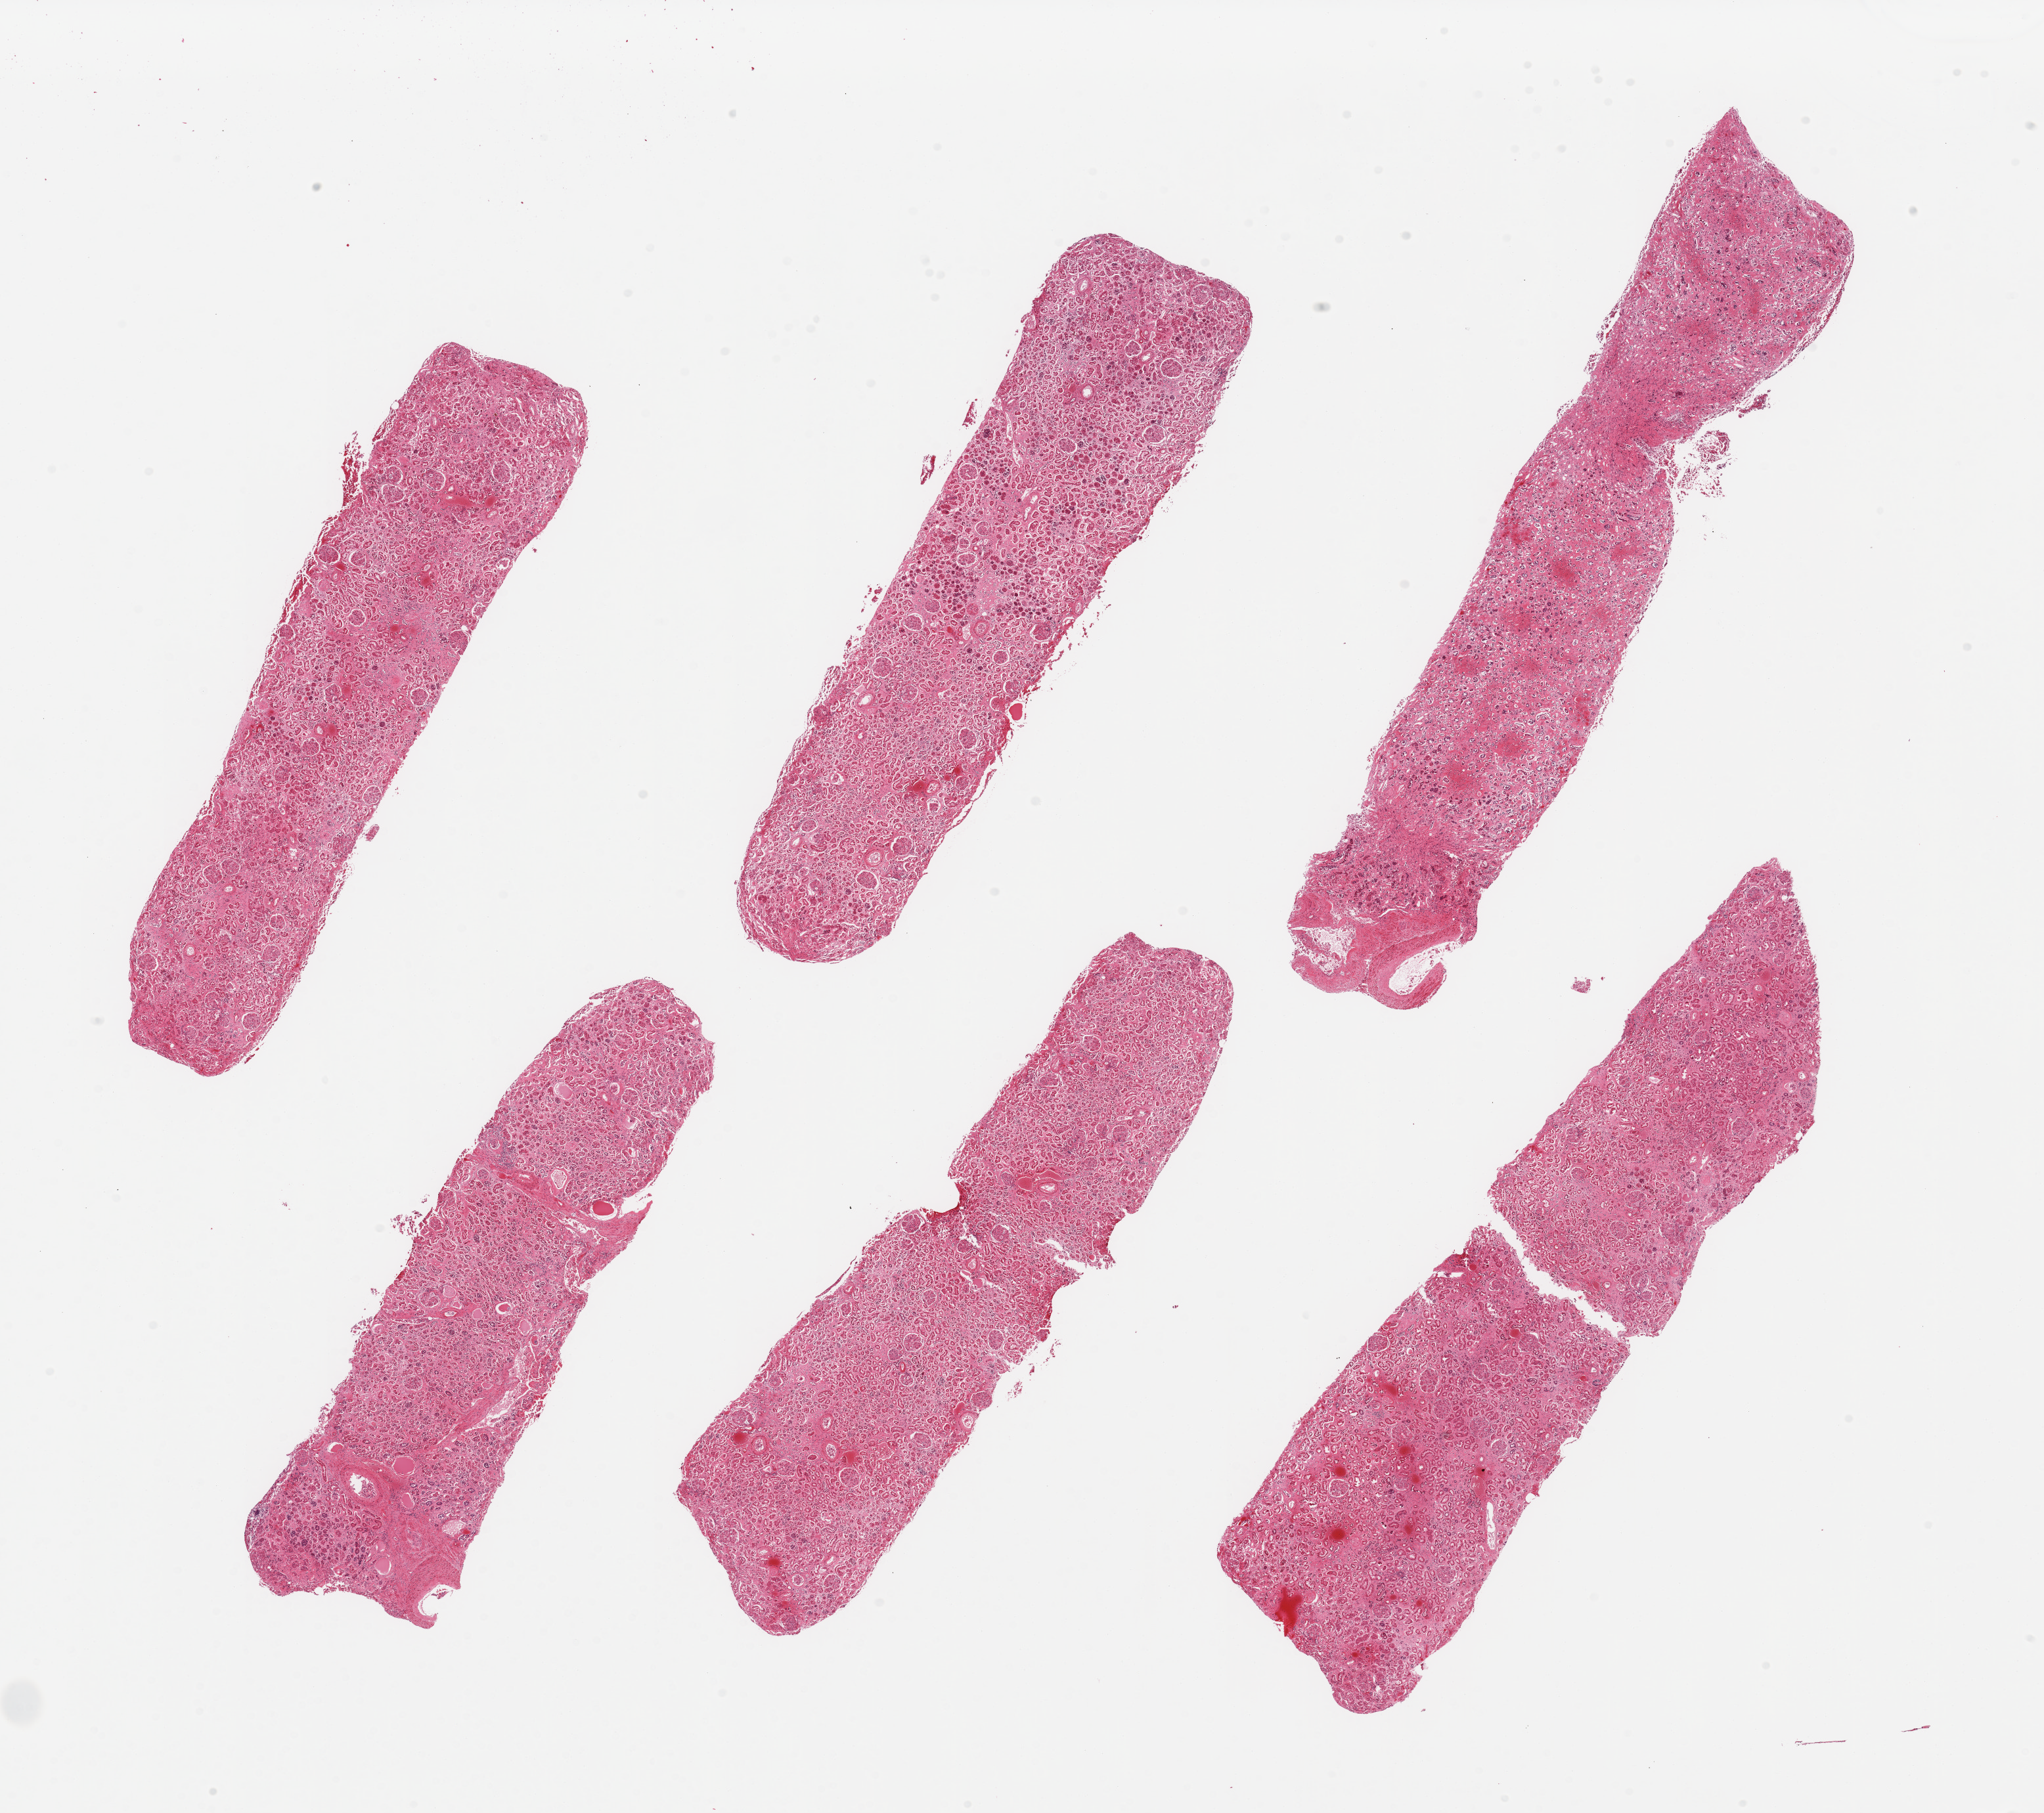
Digitized H&E-stained section — a low-resolution overview of the entire scanned area, about 24.6 x 21.8 mm. PAXgene-fixed paraffin-embedded (PFPE) section. Section of renal cortex (target tissue). Tissue donor sample.
Pathologist's review note for this sample: 6 pieces, glomeruli present, tubule with advanced autolysis.